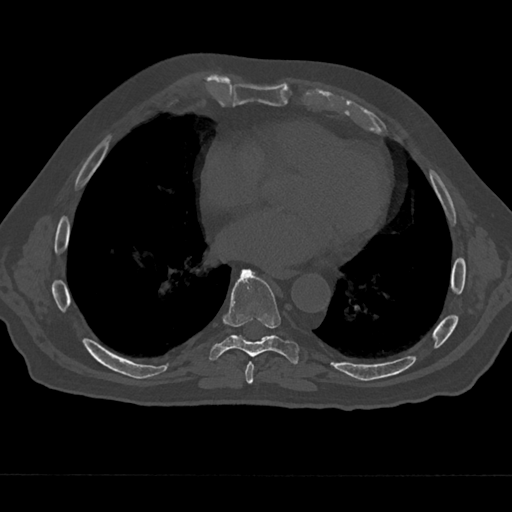
CT including the spine, one axial slice. Position 317 of 797 along the scan axis. 120 kVp. Bone window (W 1800 / L 400 HU). 0.5 mm slice thickness. 512 × 512 image matrix, field of view 377 × 377 mm. Male patient, age 75 years. From the clinical record (not read from this slice): primary cancer: renal.
Annotated regions visible in this slice (semi-automatically segmented with operator editing):
- T7 vertebra: box from (x=243, y=361) to (x=260, y=384) px
- T8 vertebra: (x=209, y=269)–(x=300, y=364)